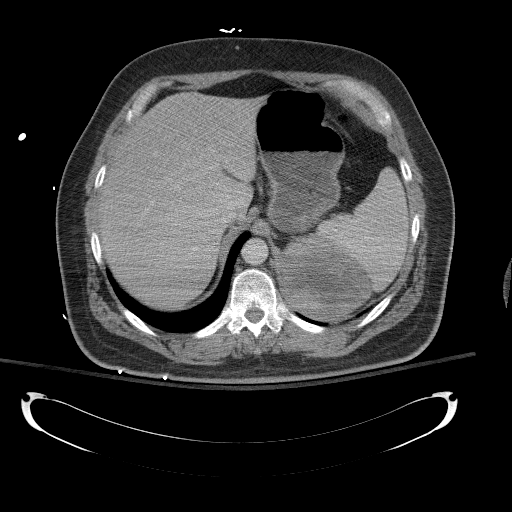
Contrast-enhanced abdominal CT, one axial slice. Slice 95 of 154 in the series (ordered by position). 120 kVp. Soft-tissue window (W 400 / L 40 HU). 5 mm slice thickness. 512 × 512 image matrix, field of view 467 × 467 mm. Patient: male, 43 years. Case-level facts recorded for this patient, not image findings: diagnosis: adrenocortical carcinoma; tumour side: left adrenal; tumour size at pathology: 9.8 cm; Ki-67 index: 30 %; stage (as recorded): 2.
Outlined on this slice (semi-automatic segmentation, software-assisted and operator-edited):
- mass: bounding box [x1, y1, x2, y2] px = [281, 236, 368, 317]